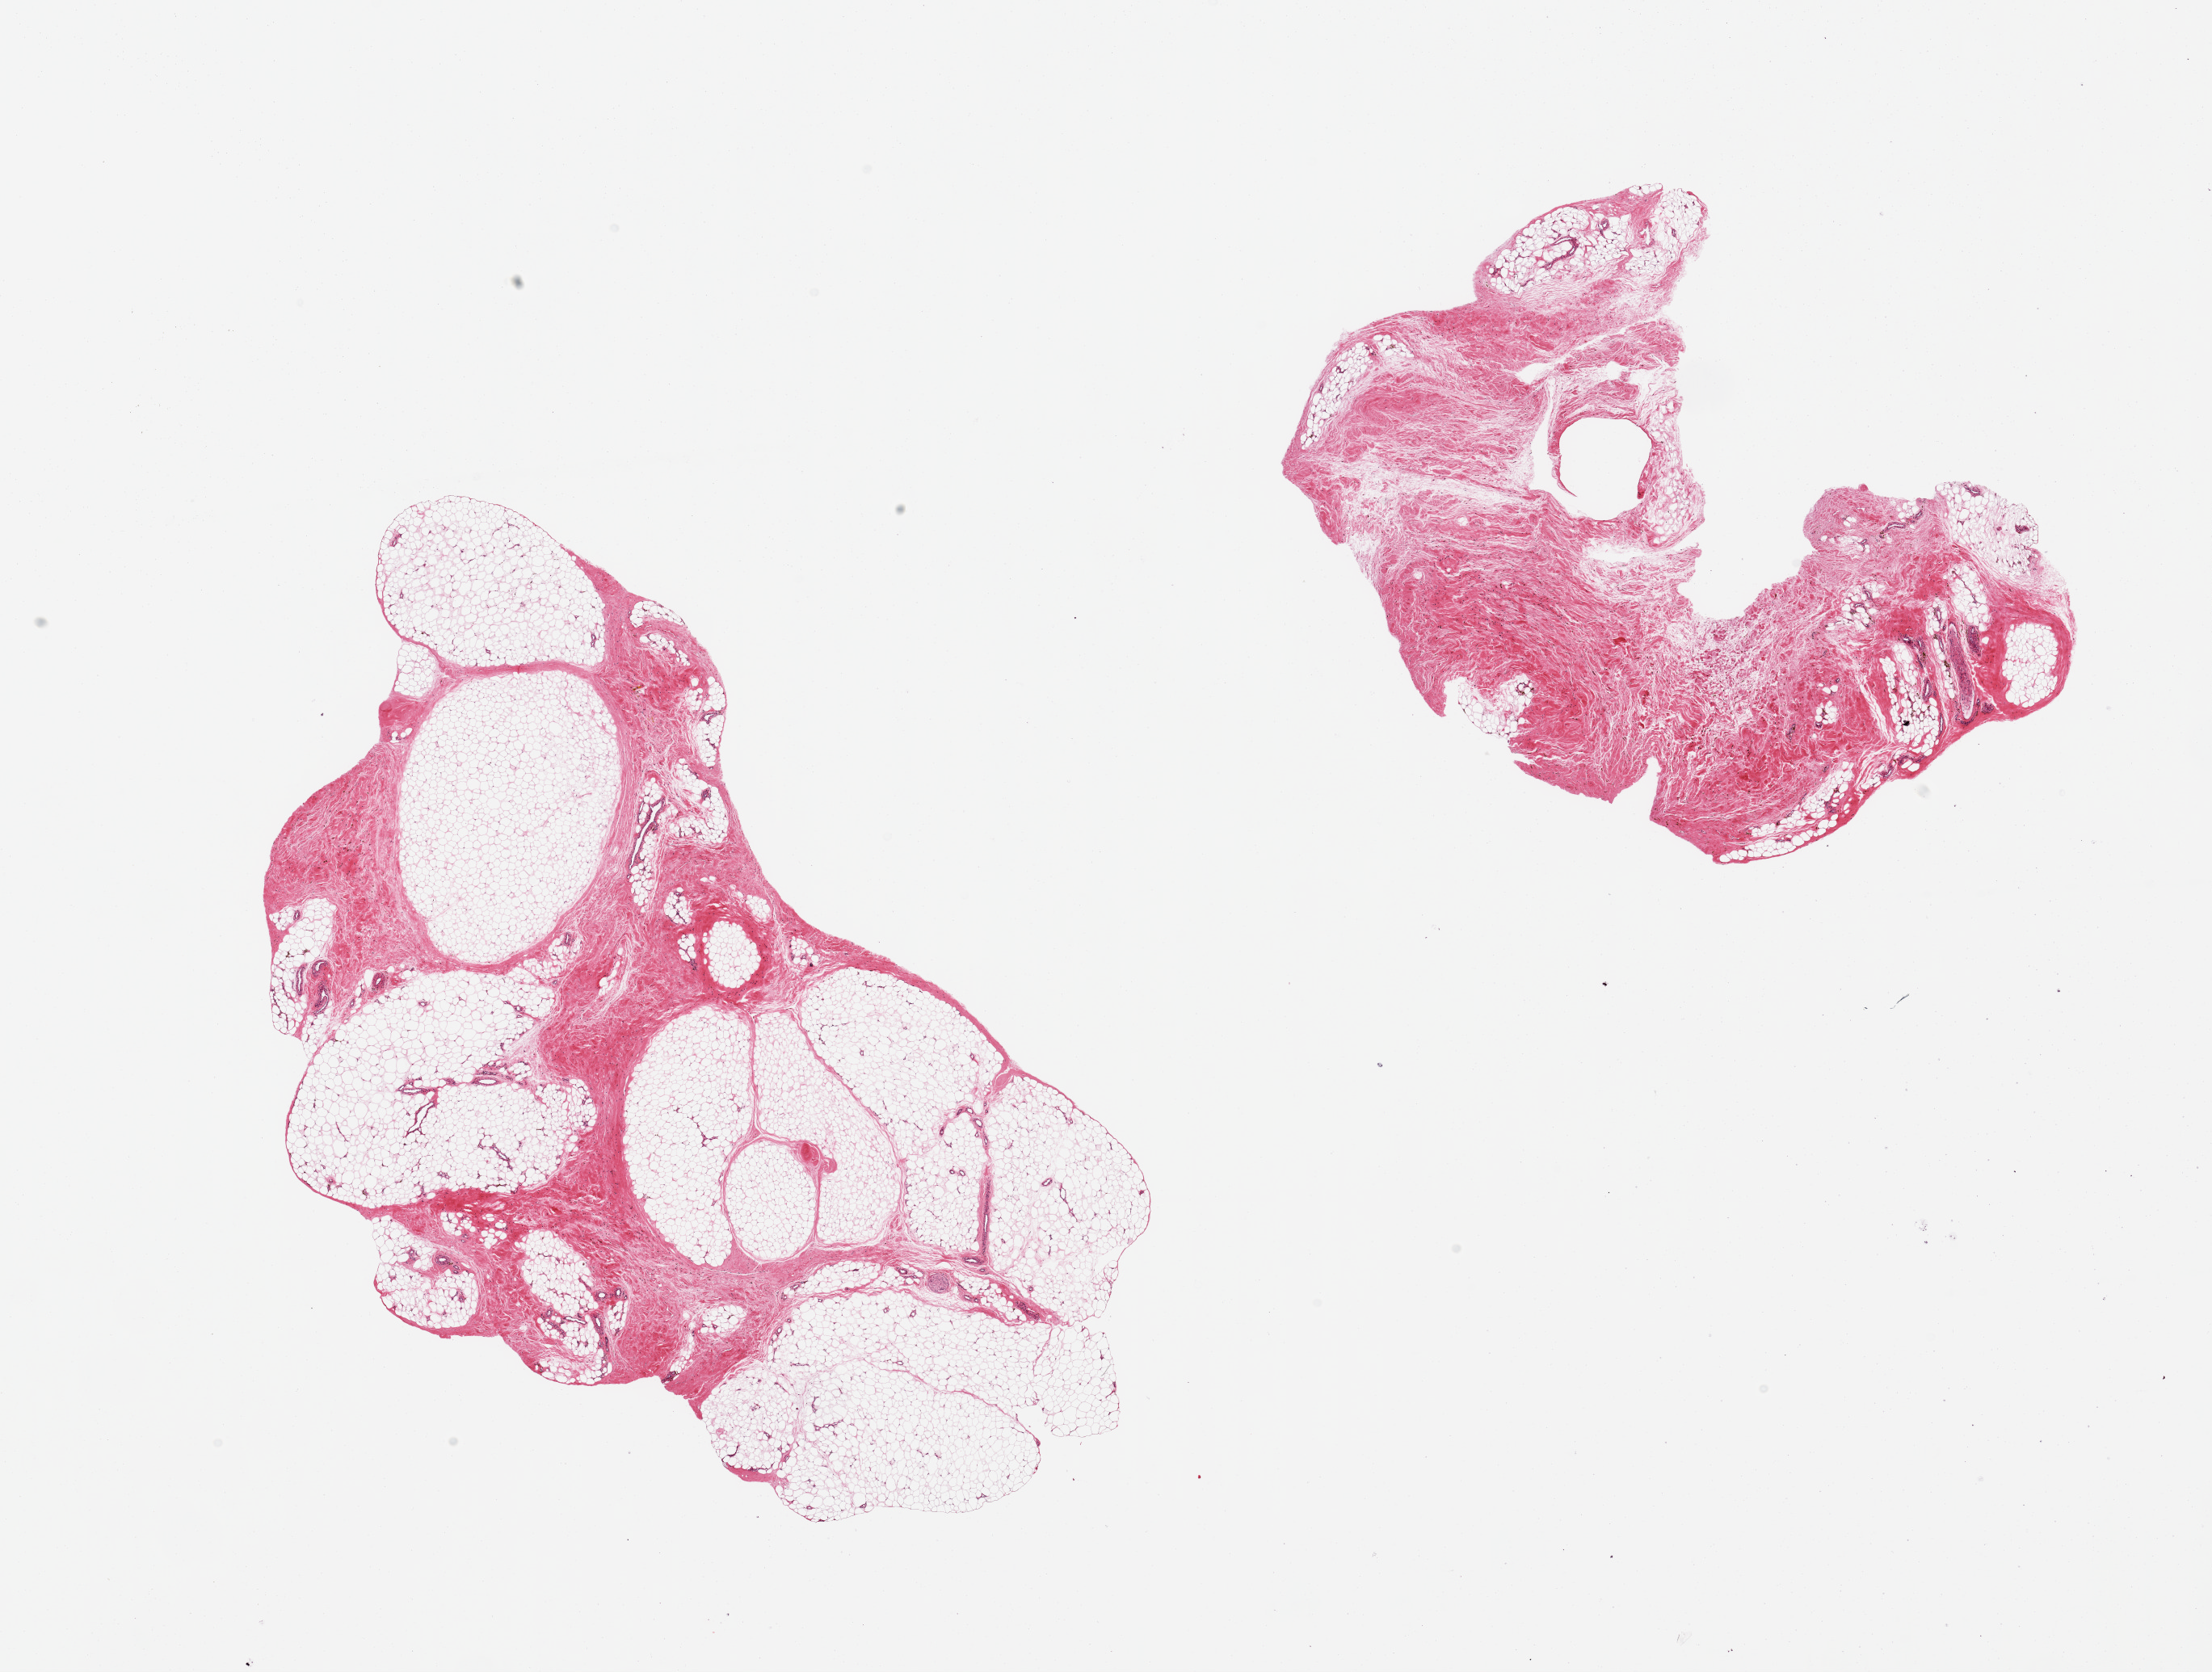
H&E whole-slide image — a low-resolution overview of the entire scanned area, about 21.7 x 16.4 mm (acquisition: 20x scan), PAXgene-fixed paraffin-embedded (PFPE) section, sampled site (target tissue): adipose tissue, donor tissue sample.
Review note (as recorded): 2 pieces; mature adipose tissue; 30% and 70% fascia and vascular elements.